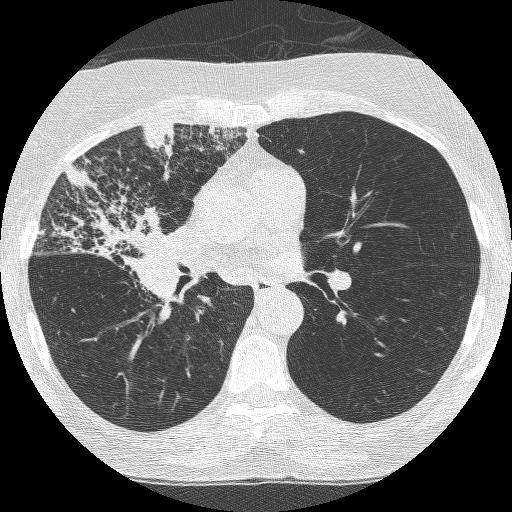
Axial slice from a low-dose chest CT screening exam, third screening round (two years after baseline), lung window (W 1500 / L -600 HU), 1.25 mm slice thickness, lung (sharp) reconstruction kernel (BONE), slice 142 of 253 in the series. Female participant, aged 64 years at enrolment. Former smoker at enrolment.
Expert reader's lesion annotation, bounding box (x1, y1, x2, y2) in pixels: (63, 175, 201, 315). Screening reader's record for this exam (one nodule recorded; not confirmed to be the boxed lesion): non-calcified nodule or mass ≥4 mm, right upper lobe, 49 × 43 mm, spiculated (stellate) margins, soft tissue attenuation, pre-existing on the prior screen: yes; interval growth: yes. Official screen result: positive, other. Lung cancer was diagnosed 7 days after this screen: adenocarcinoma, NOS, right upper lobe, right middle lobe, right hilum, stage IV (AJCC 6th edition), 85 mm at pathology.